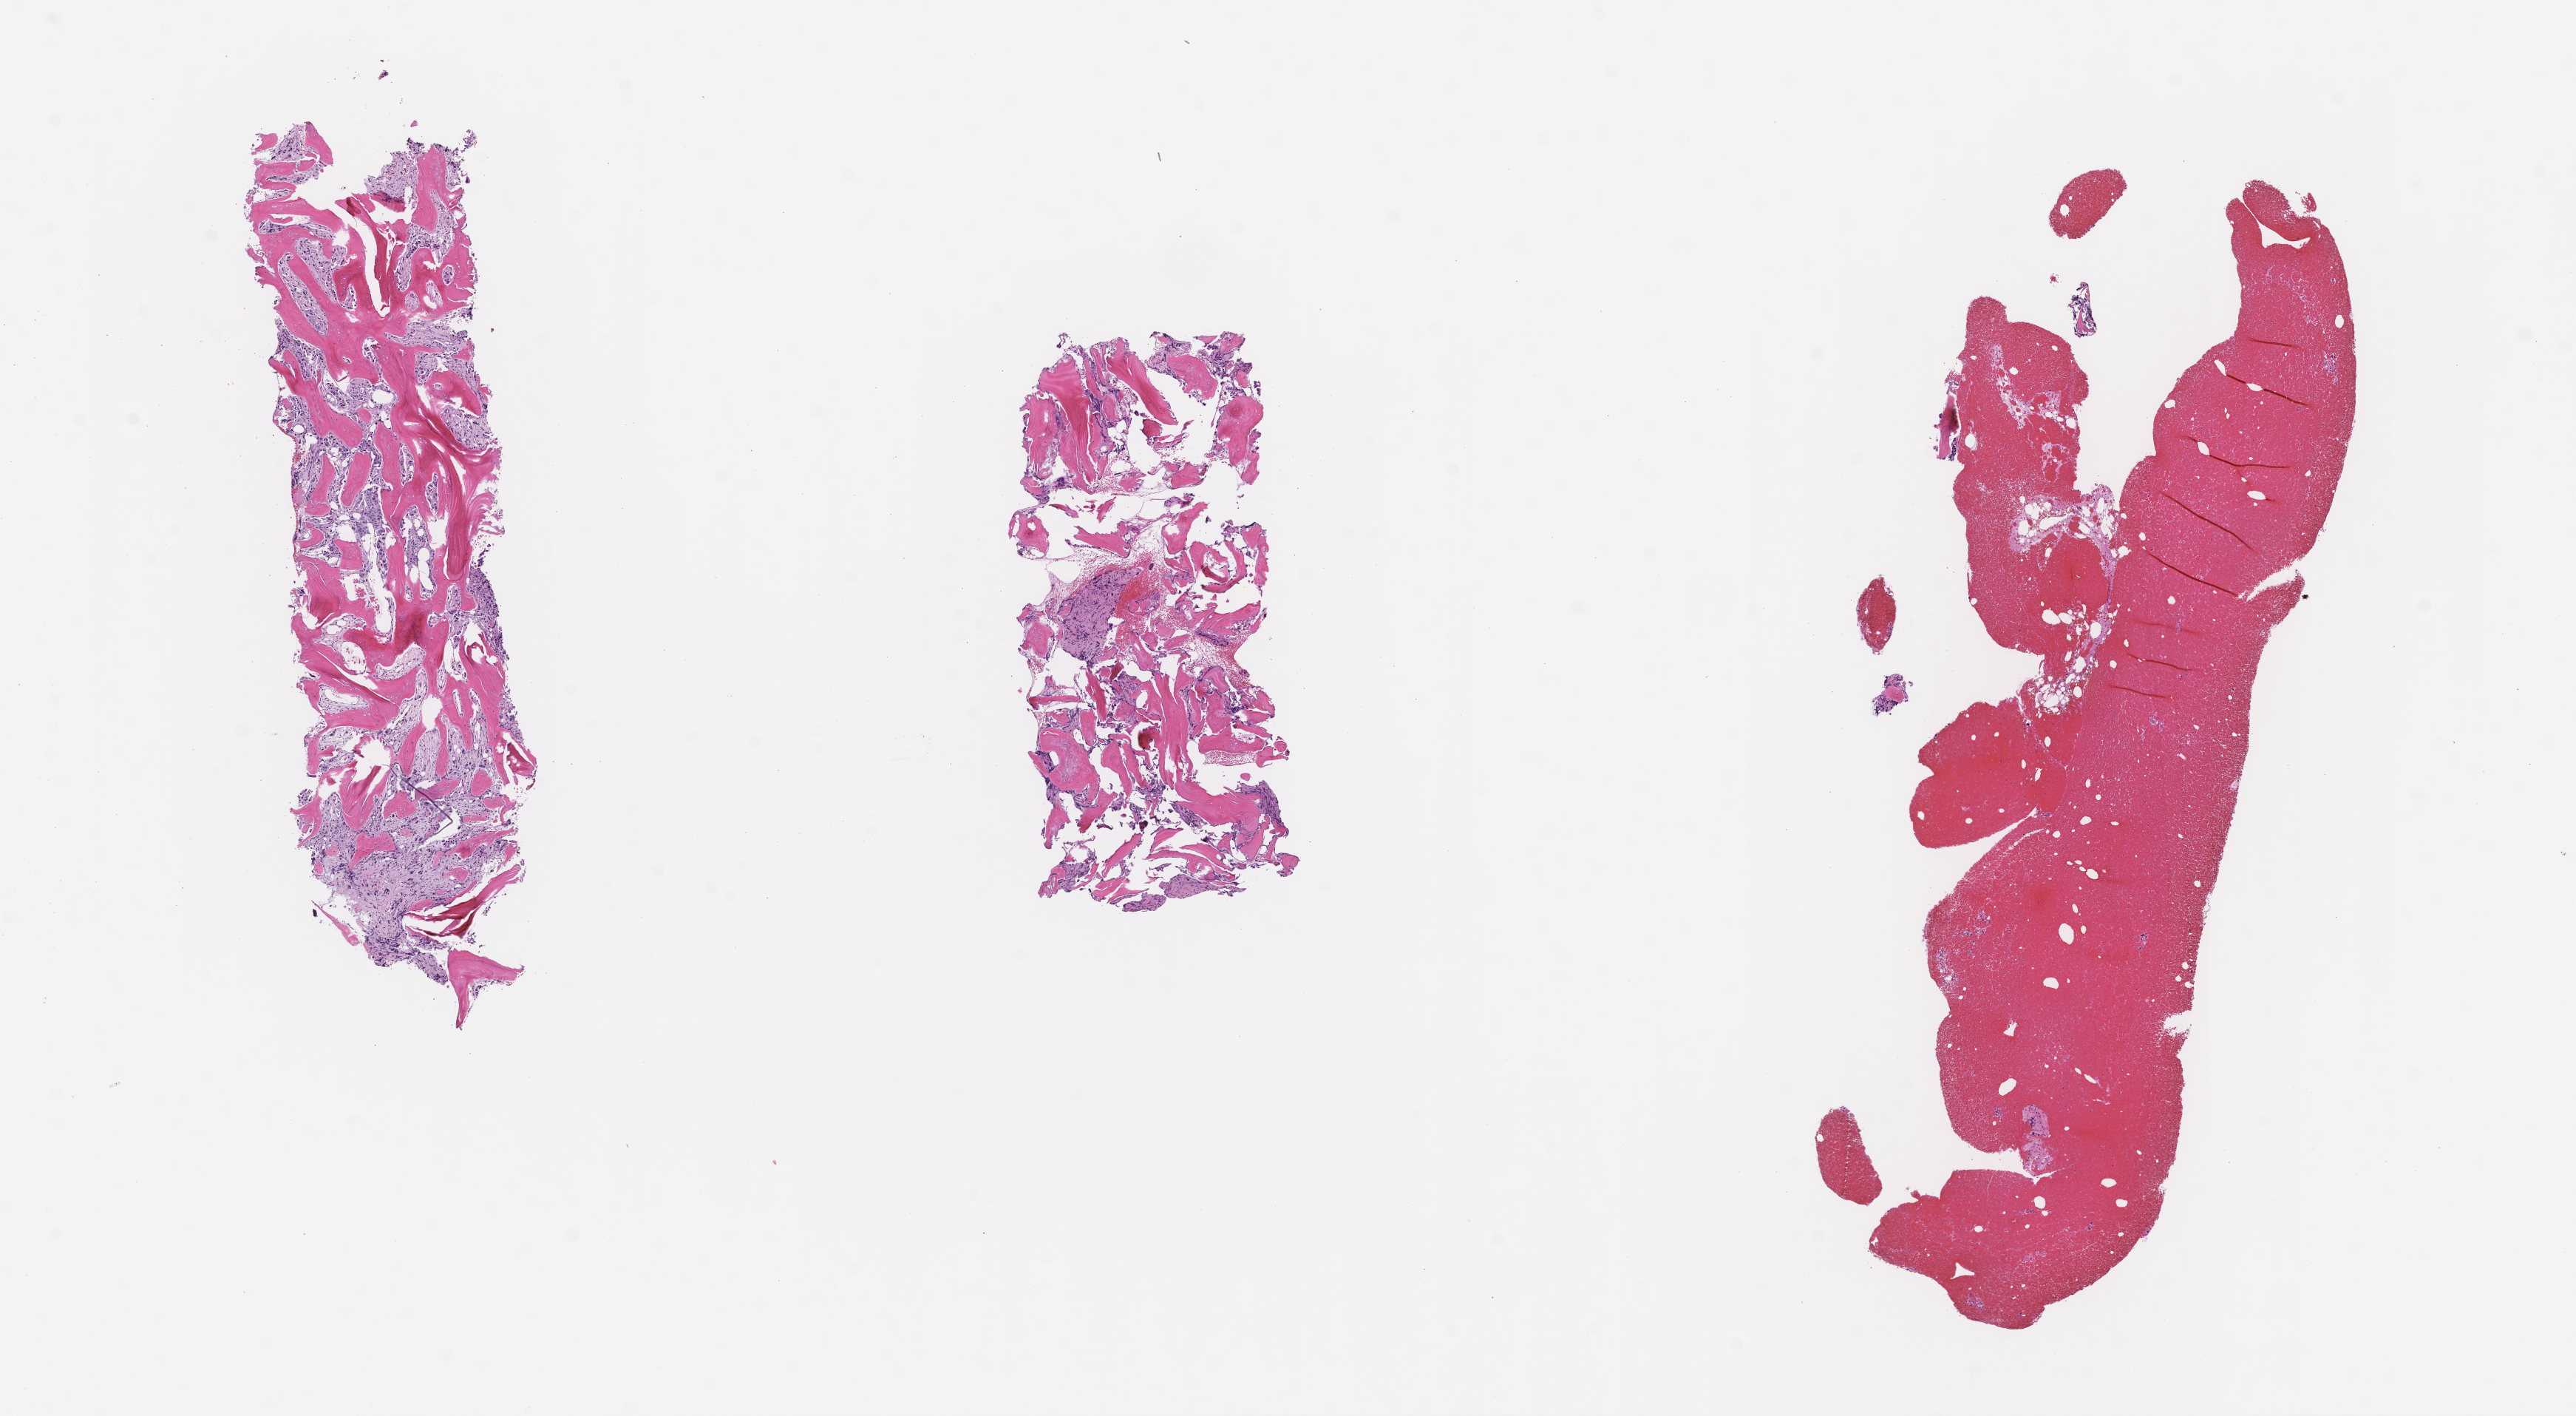
Whole-slide image, hematoxylin and eosin (H&E) stain, a low-resolution overview of the entire scanned area, about 14.1 x 7.7 mm. Formalin-fixed, paraffin-embedded (FFPE) tissue. Specimen time point: collected at disease progression. Patient sex: female.
This section: metastasis (sampled organ not recorded). Patient diagnosis (primary): Invasive Breast Carcinoma.